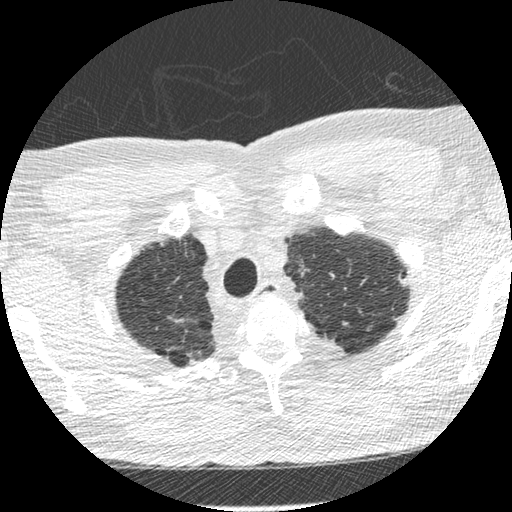
Low-dose screening chest CT, one axial slice; position 245 of 275 along the scan axis; lung window (W 1500 / L -600 HU); 1.25 mm slice thickness; 512 × 512 image matrix.
Outlined on this slice (outlined manually by an expert reader):
- lesion 1 (tumor, upper lobe of left lung): box from (x=398, y=274) to (x=408, y=287) px